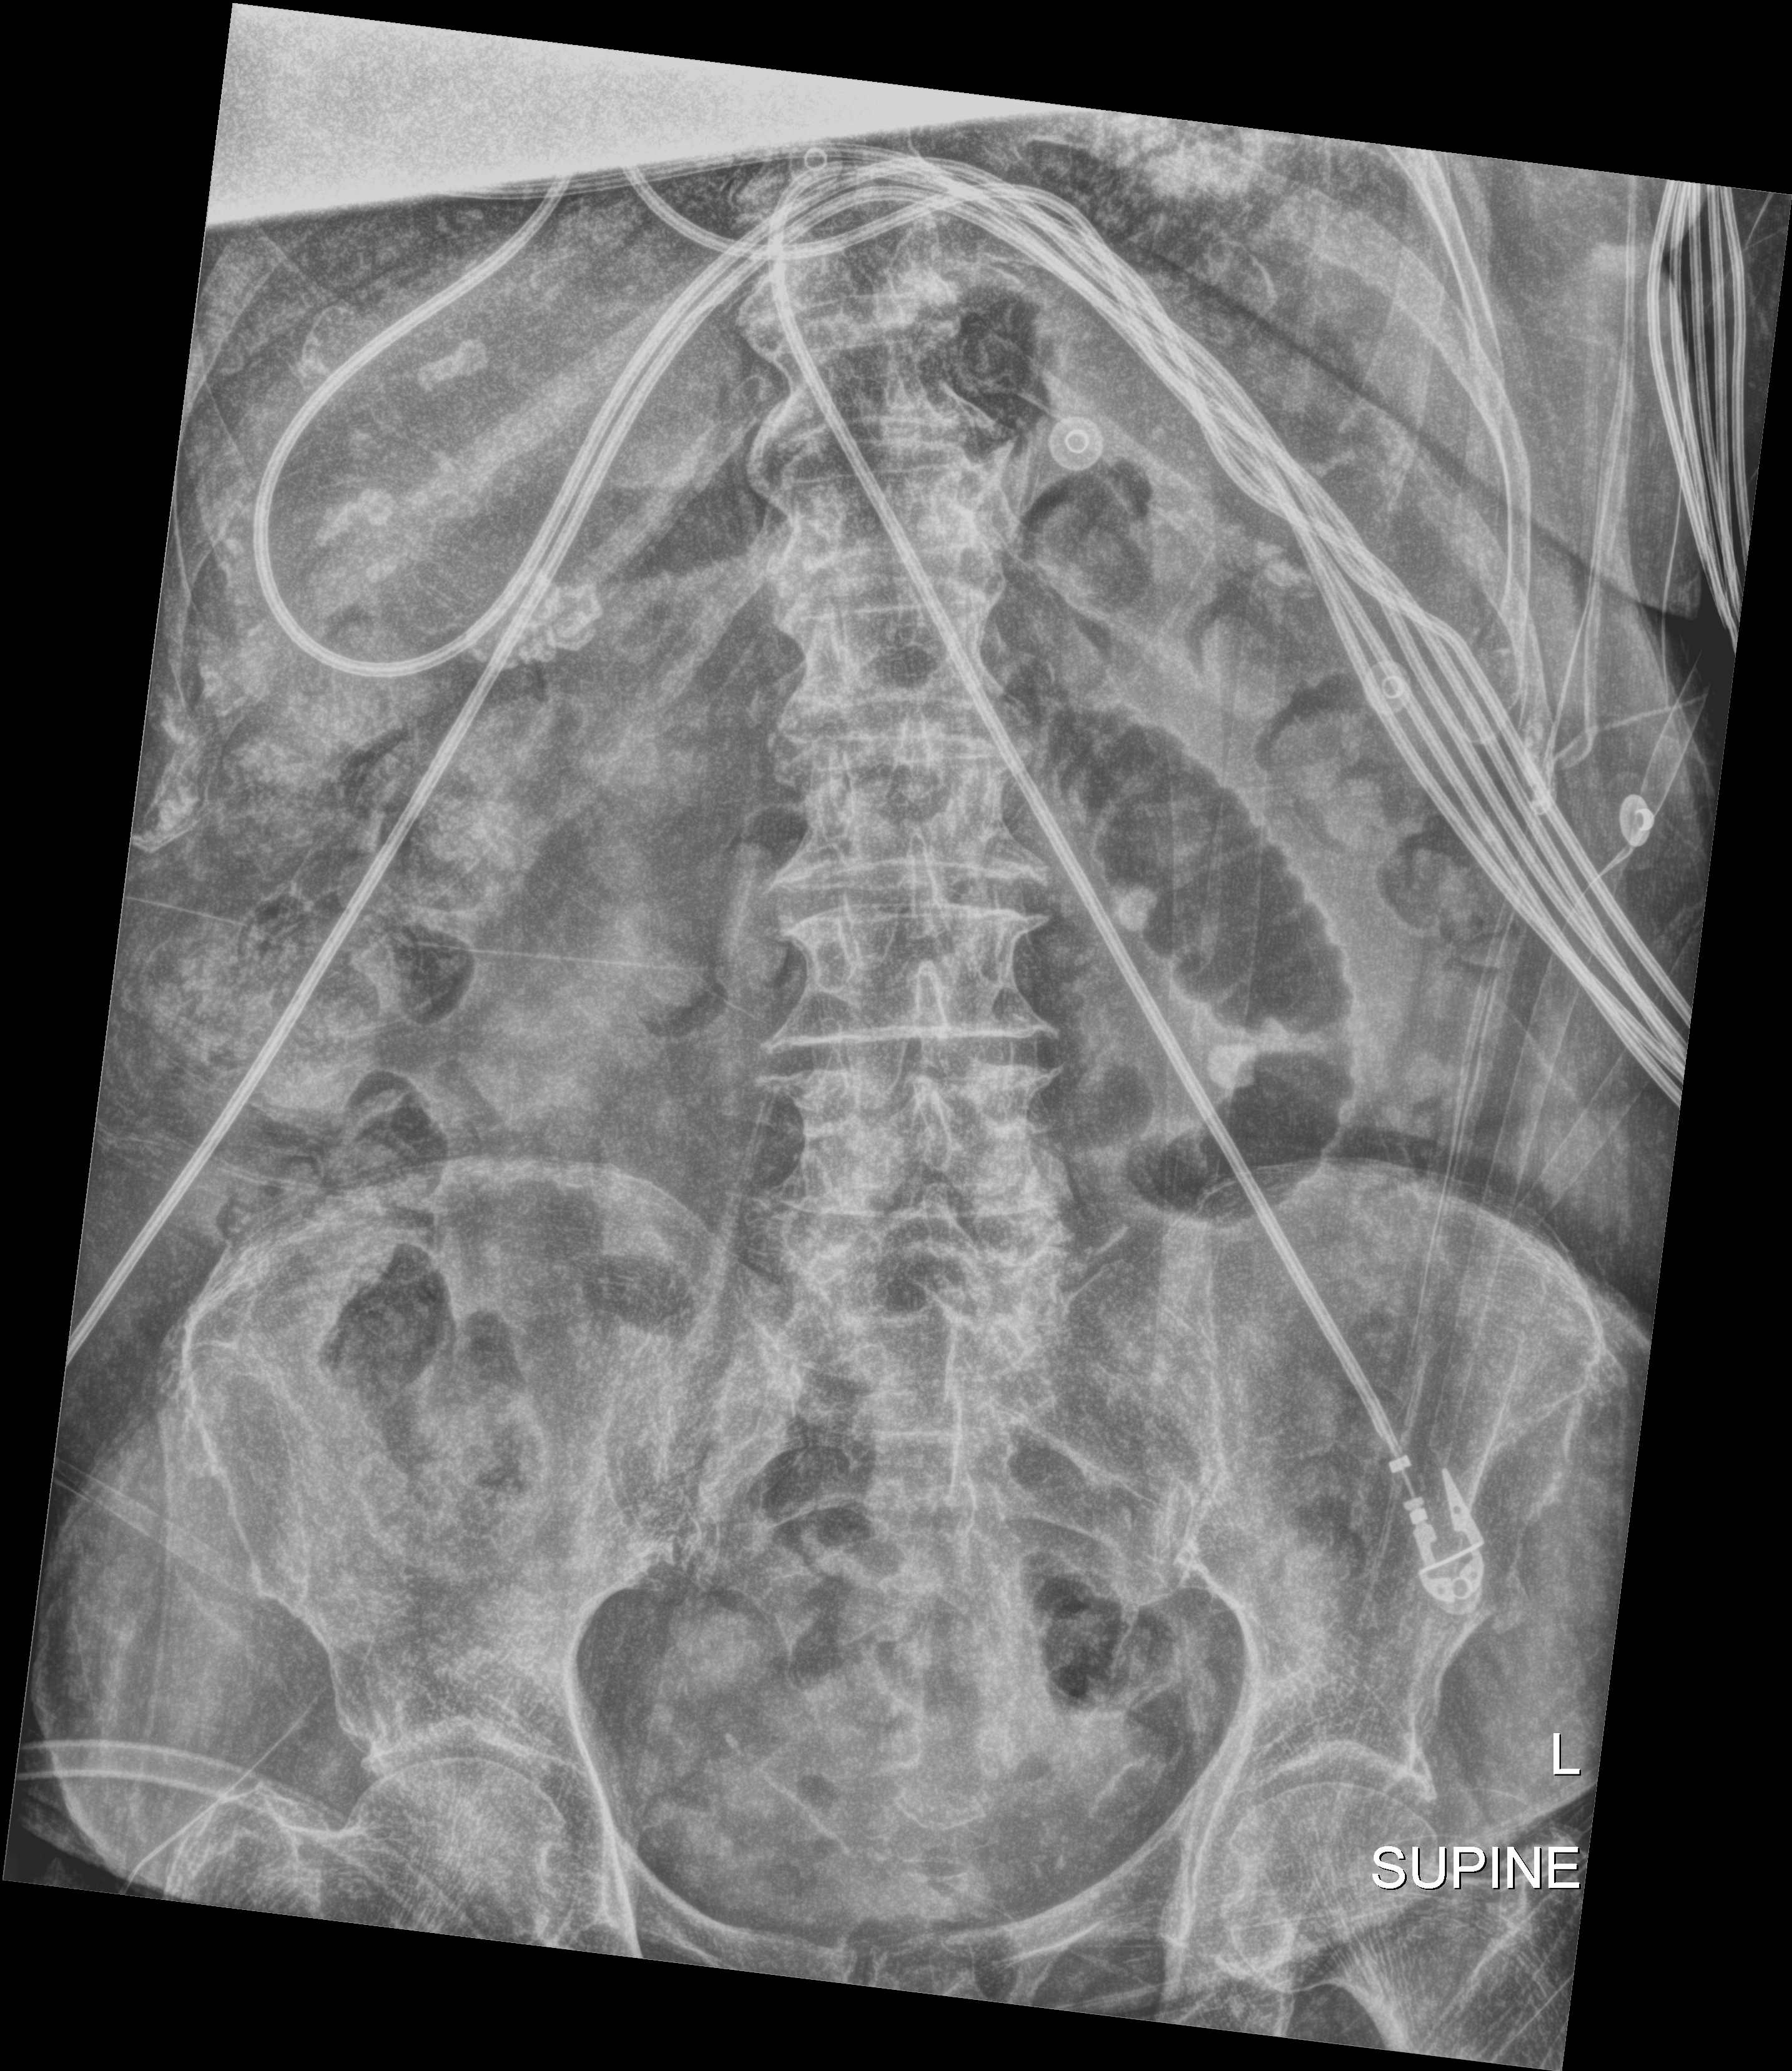
Abdomen X-ray (portable), anteroposterior (AP) projection. Patient hospitalised with COVID-19; female, aged 75–90 years.
Admission-level facts for this patient (not findings on this image; timing relative to this image not recorded): admitted to intensive care during this hospital stay: no; mechanically ventilated during this hospital stay: no.